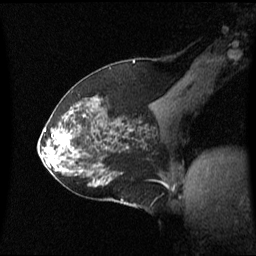
Breast MRI (dynamic contrast-enhanced), one sagittal slice; slice 34 of 60 in the series (ordered by position); dynamic contrast-enhanced series, image 2 of 3 at this slice position (ordered by acquisition); 1.5 T; TE 4.2 ms, TR 8.4 ms; 2 mm slice thickness; 256 × 256 image matrix, field of view 240 × 240 mm. Female patient, age 59 years. From the clinical record (not read from this slice): setting: breast cancer imaged before/during neoadjuvant chemotherapy; receptor status: HR-positive, HER2-negative.
Structures marked on this image (semi-automatic segmentation, software-assisted and operator-edited):
- analysis volume of interest (the breast-tissue region the enhancement analysis was run in; not a lesion): bounding box [x1, y1, x2, y2] px = [46, 114, 85, 163]
- tumour enhancement mask (voxels above the 70 % enhancement threshold inside the analysis volume of interest): [58, 134, 68, 143]